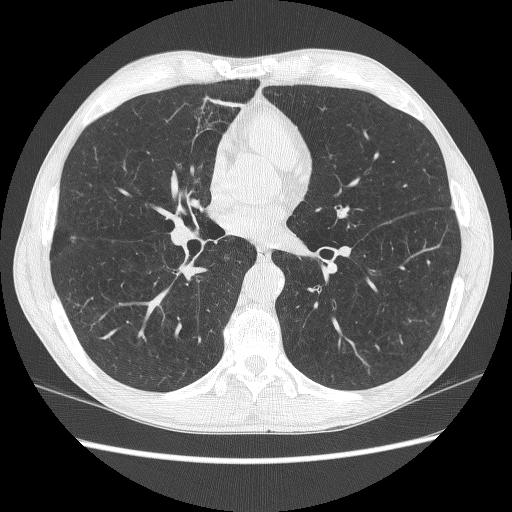
Axial slice from a low-dose chest CT screening exam, baseline screening round, lung window (W 1500 / L -600 HU), lung (sharp) reconstruction kernel (BONE), 120 kVp, slice 125 of 278 in the series. Male participant, aged 62 years at enrolment. Former smoker at enrolment.
- Lesion marked by an expert reader, bounding box (x1, y1, x2, y2) in pixels: (326, 204, 362, 241).
- The exam's reader record, not a measurement of the box and not confirmed to be the same lesion: non-calcified nodule or mass ≥4 mm, right lower lobe, 8 × 4 mm, poorly defined margins, soft tissue attenuation, pre-existing on the prior screen: no.
- Note: the box lies in the patient's left hemithorax on this image, whereas the reader's record names the right lung; they may be different findings.
- Participant outcome: lung cancer diagnosed 452 days after this screen — small cell carcinoma, NOS, left upper lobe, stage IIIA (AJCC 6th edition).